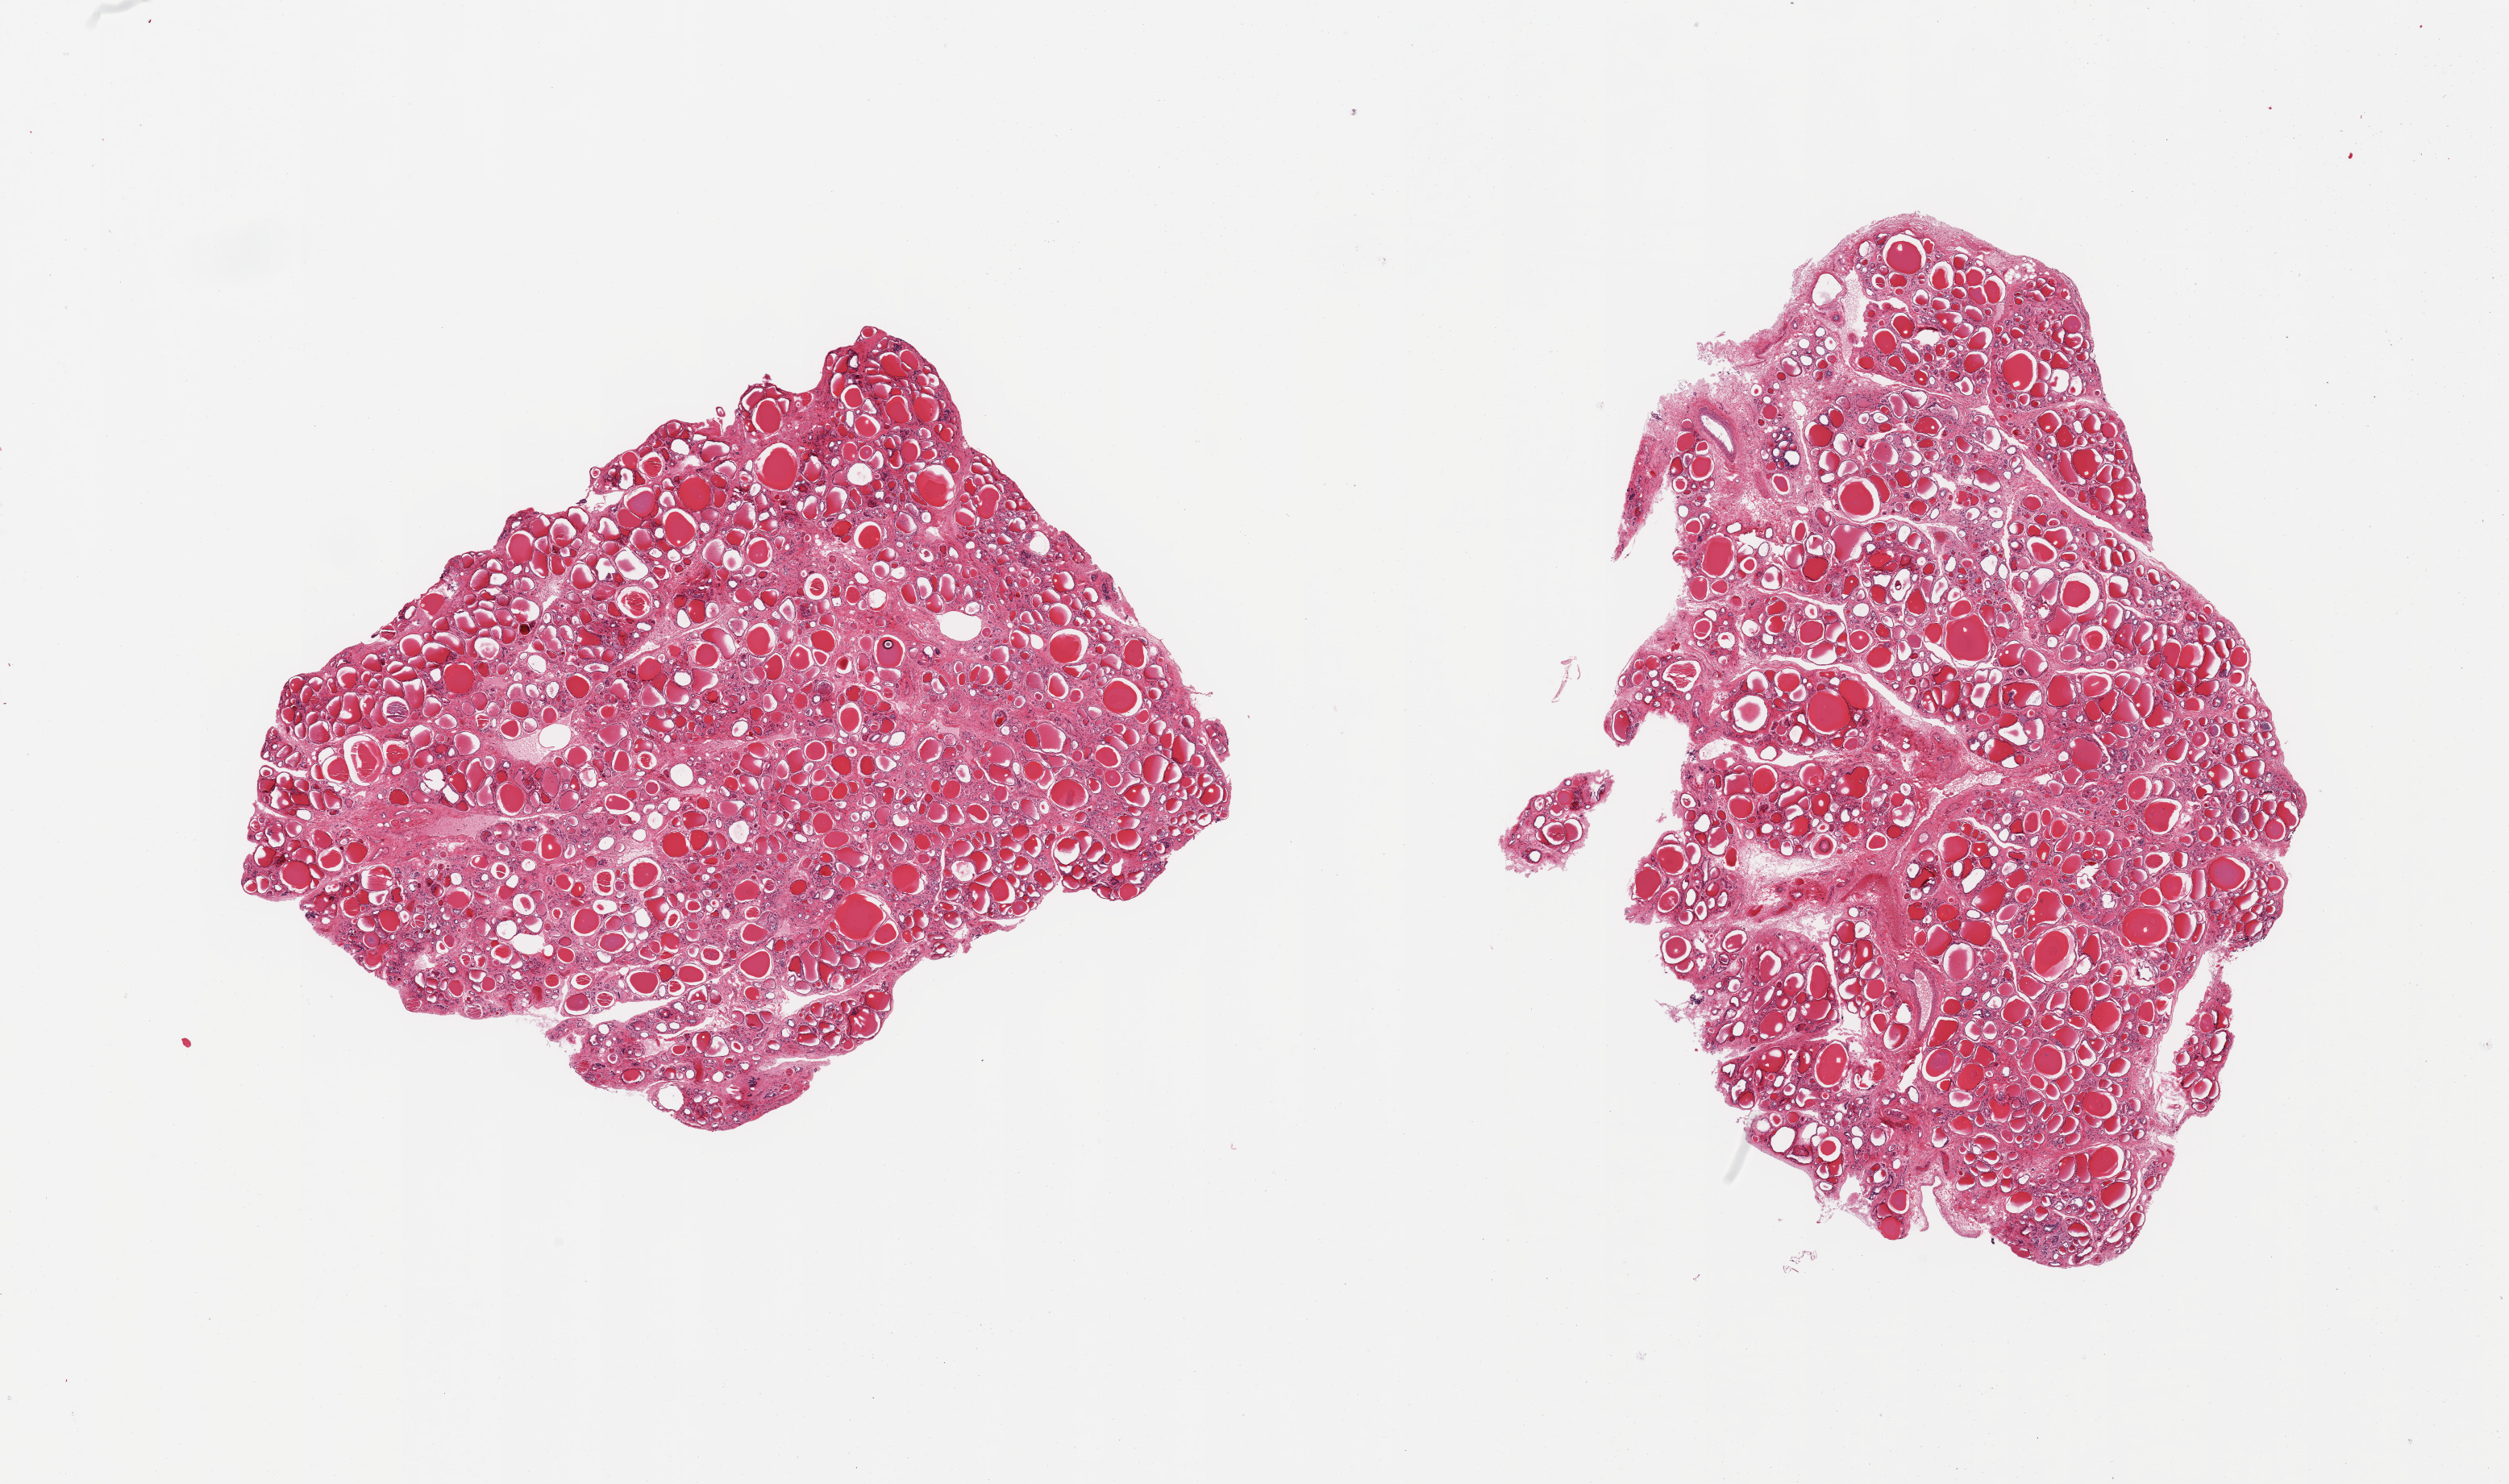
H&E whole-slide image — a low-resolution overview of the entire scanned area, about 24.6 x 14.6 mm, PAXgene-fixed paraffin-embedded (PFPE) section, sampled site (target tissue): thyroid, donor tissue sample. Male donor.
Review note (as recorded): 2 pieces of thyroid tissue; interstitial fibrosis.